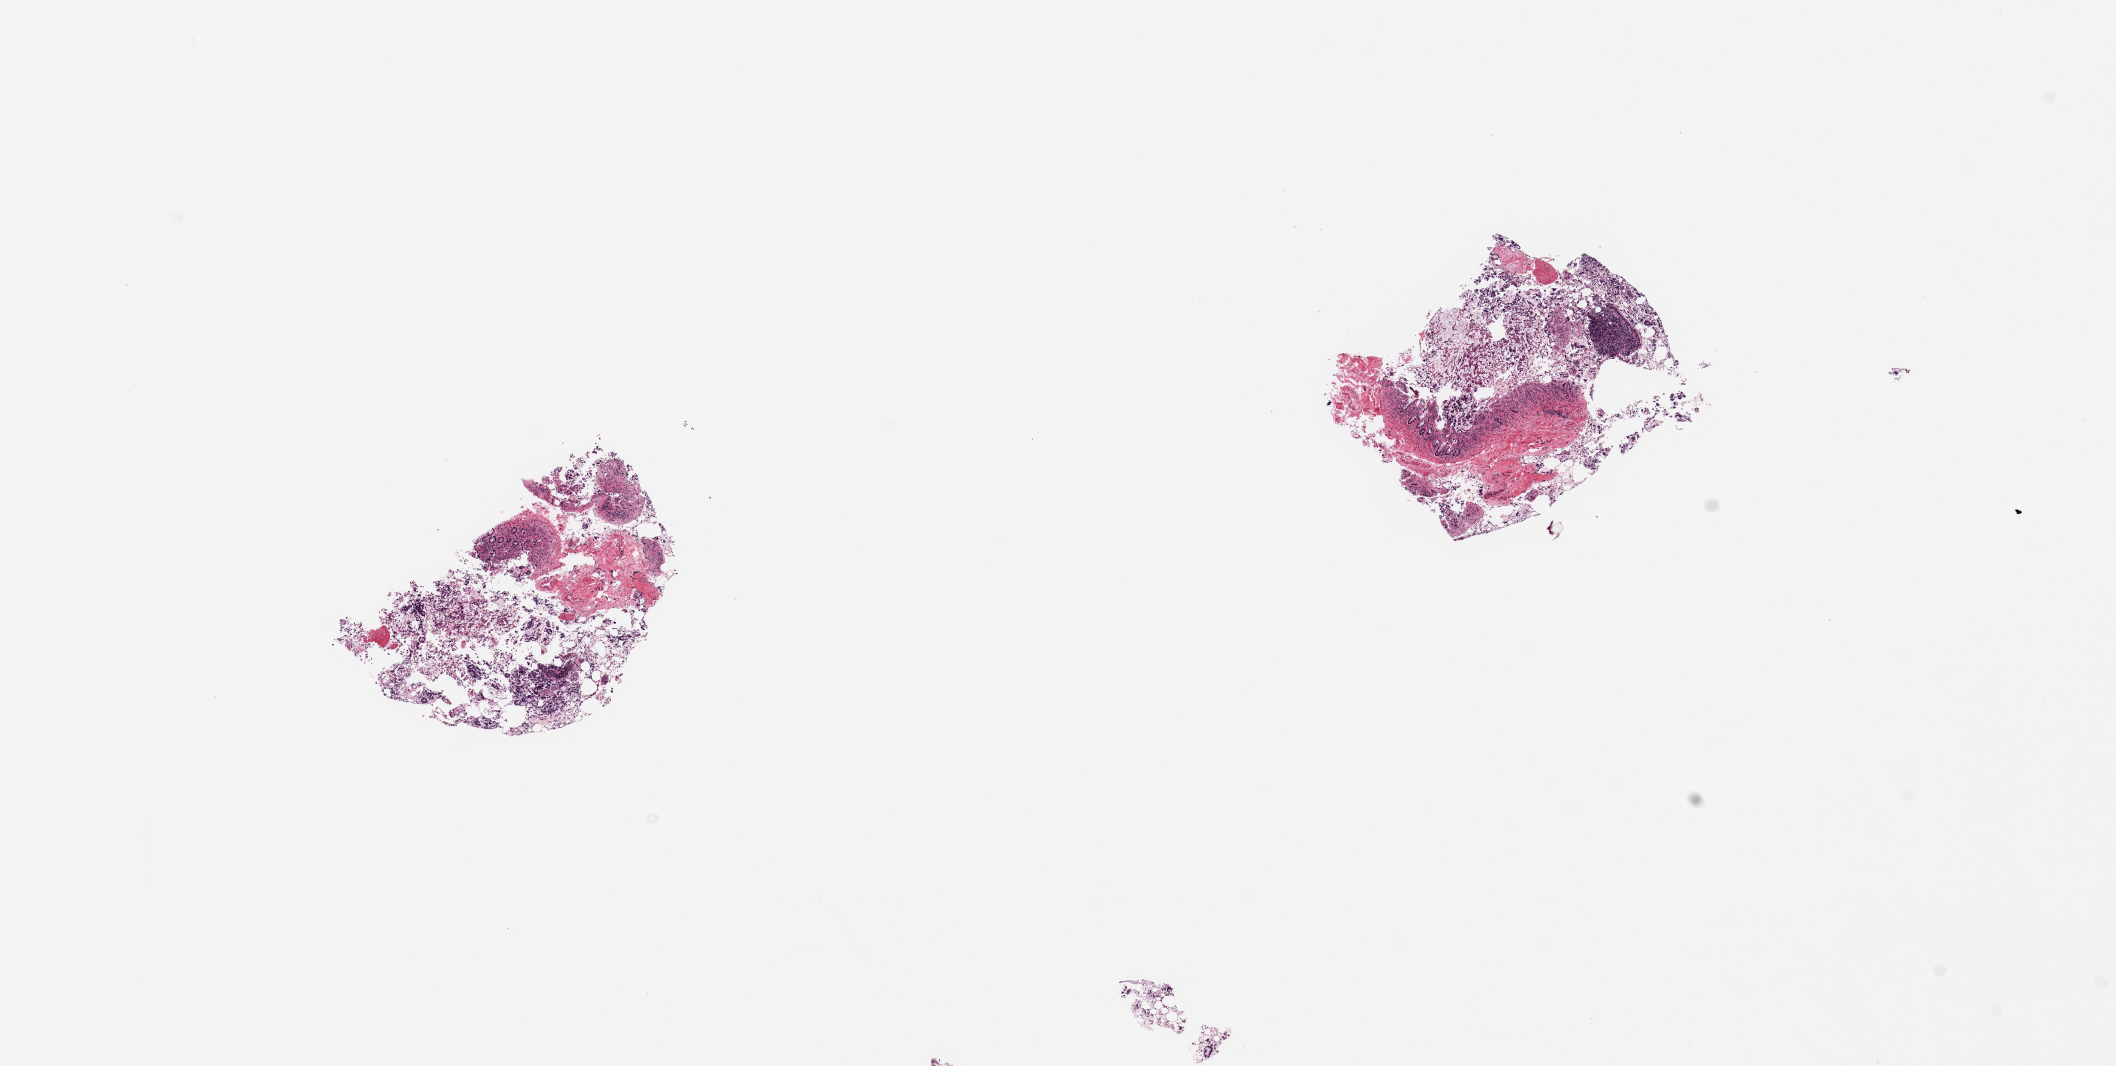
Digitized hematoxylin and eosin (H&E)-stained section — low-resolution overview of the scanned area, about 16.7 x 8.4 mm. Donor: female.
Specimen: PAXgene-fixed paraffin-embedded (PFPE) section; sampled site (target tissue): ileum; tissue donor sample.